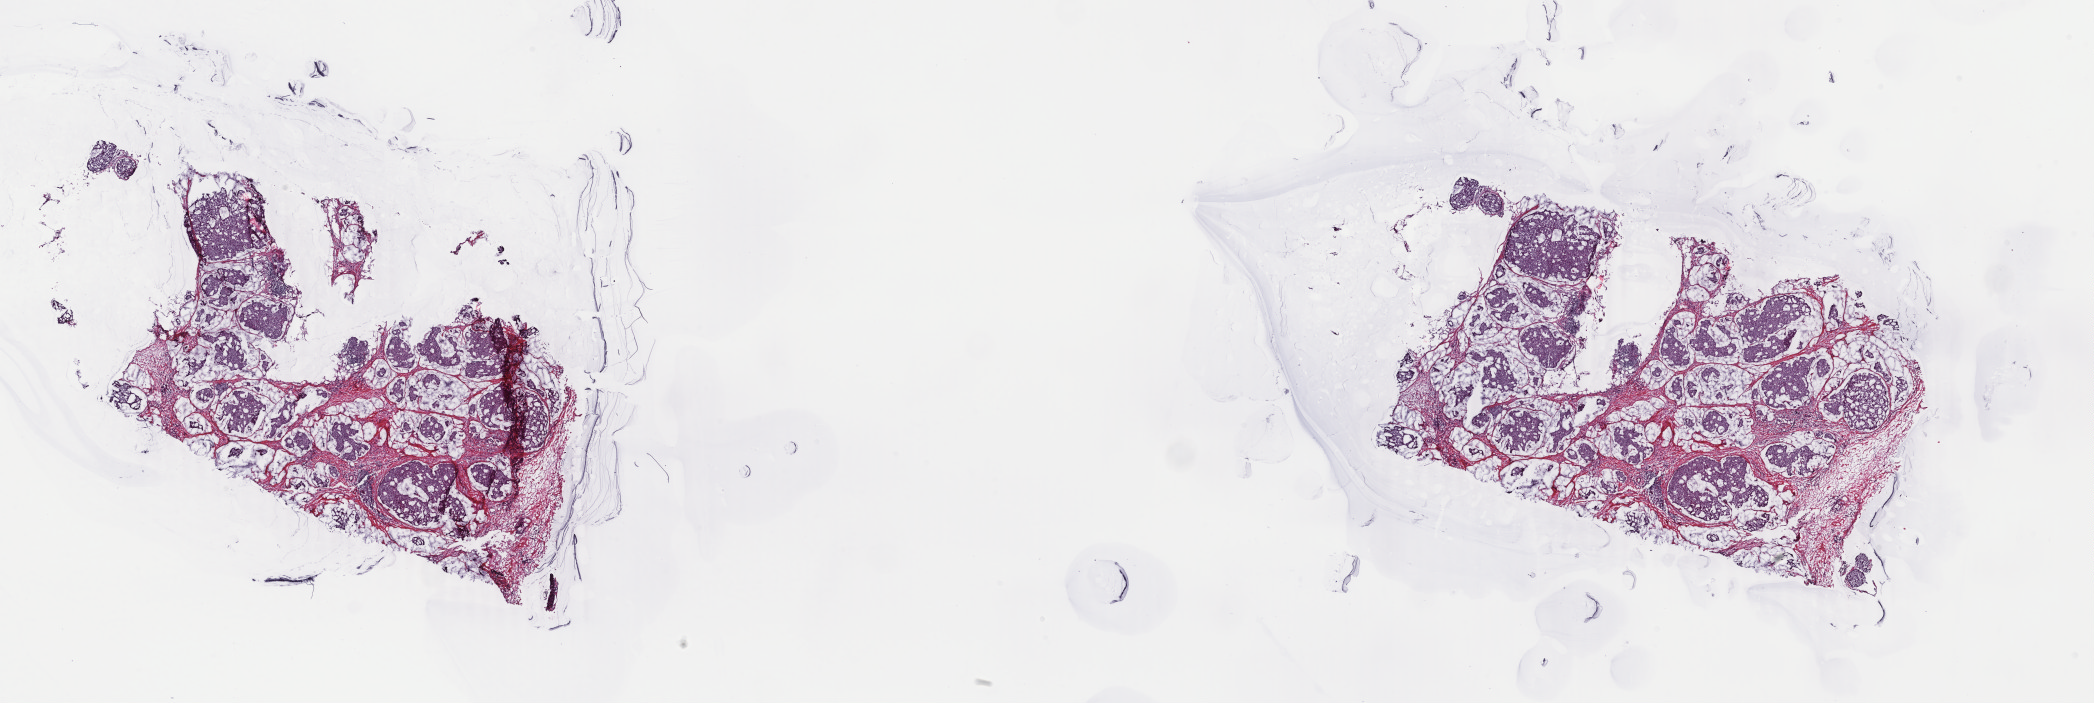
H&E whole-slide image — low-resolution overview of the scanned area, about 33.3 x 11.2 mm (acquisition: 40x scan); frozen section; primary tumour sample from the breast. Female patient; age at initial diagnosis 71 years. Pathologist review of this section (percent, as recorded): tumour cells 100%, tumour nuclei 90%, normal cells 0%, stromal cells 0%, necrosis 0%. Infiltration values recorded for this section: lymphocyte infiltration 0%, monocyte infiltration 0%, neutrophil infiltration 0%.
Diagnosis: Infiltrating duct carcinoma, NOS. Lymph nodes positive (case pathology): 2 of 15 examined. AJCC pathologic stage: IIIA (7th edition).